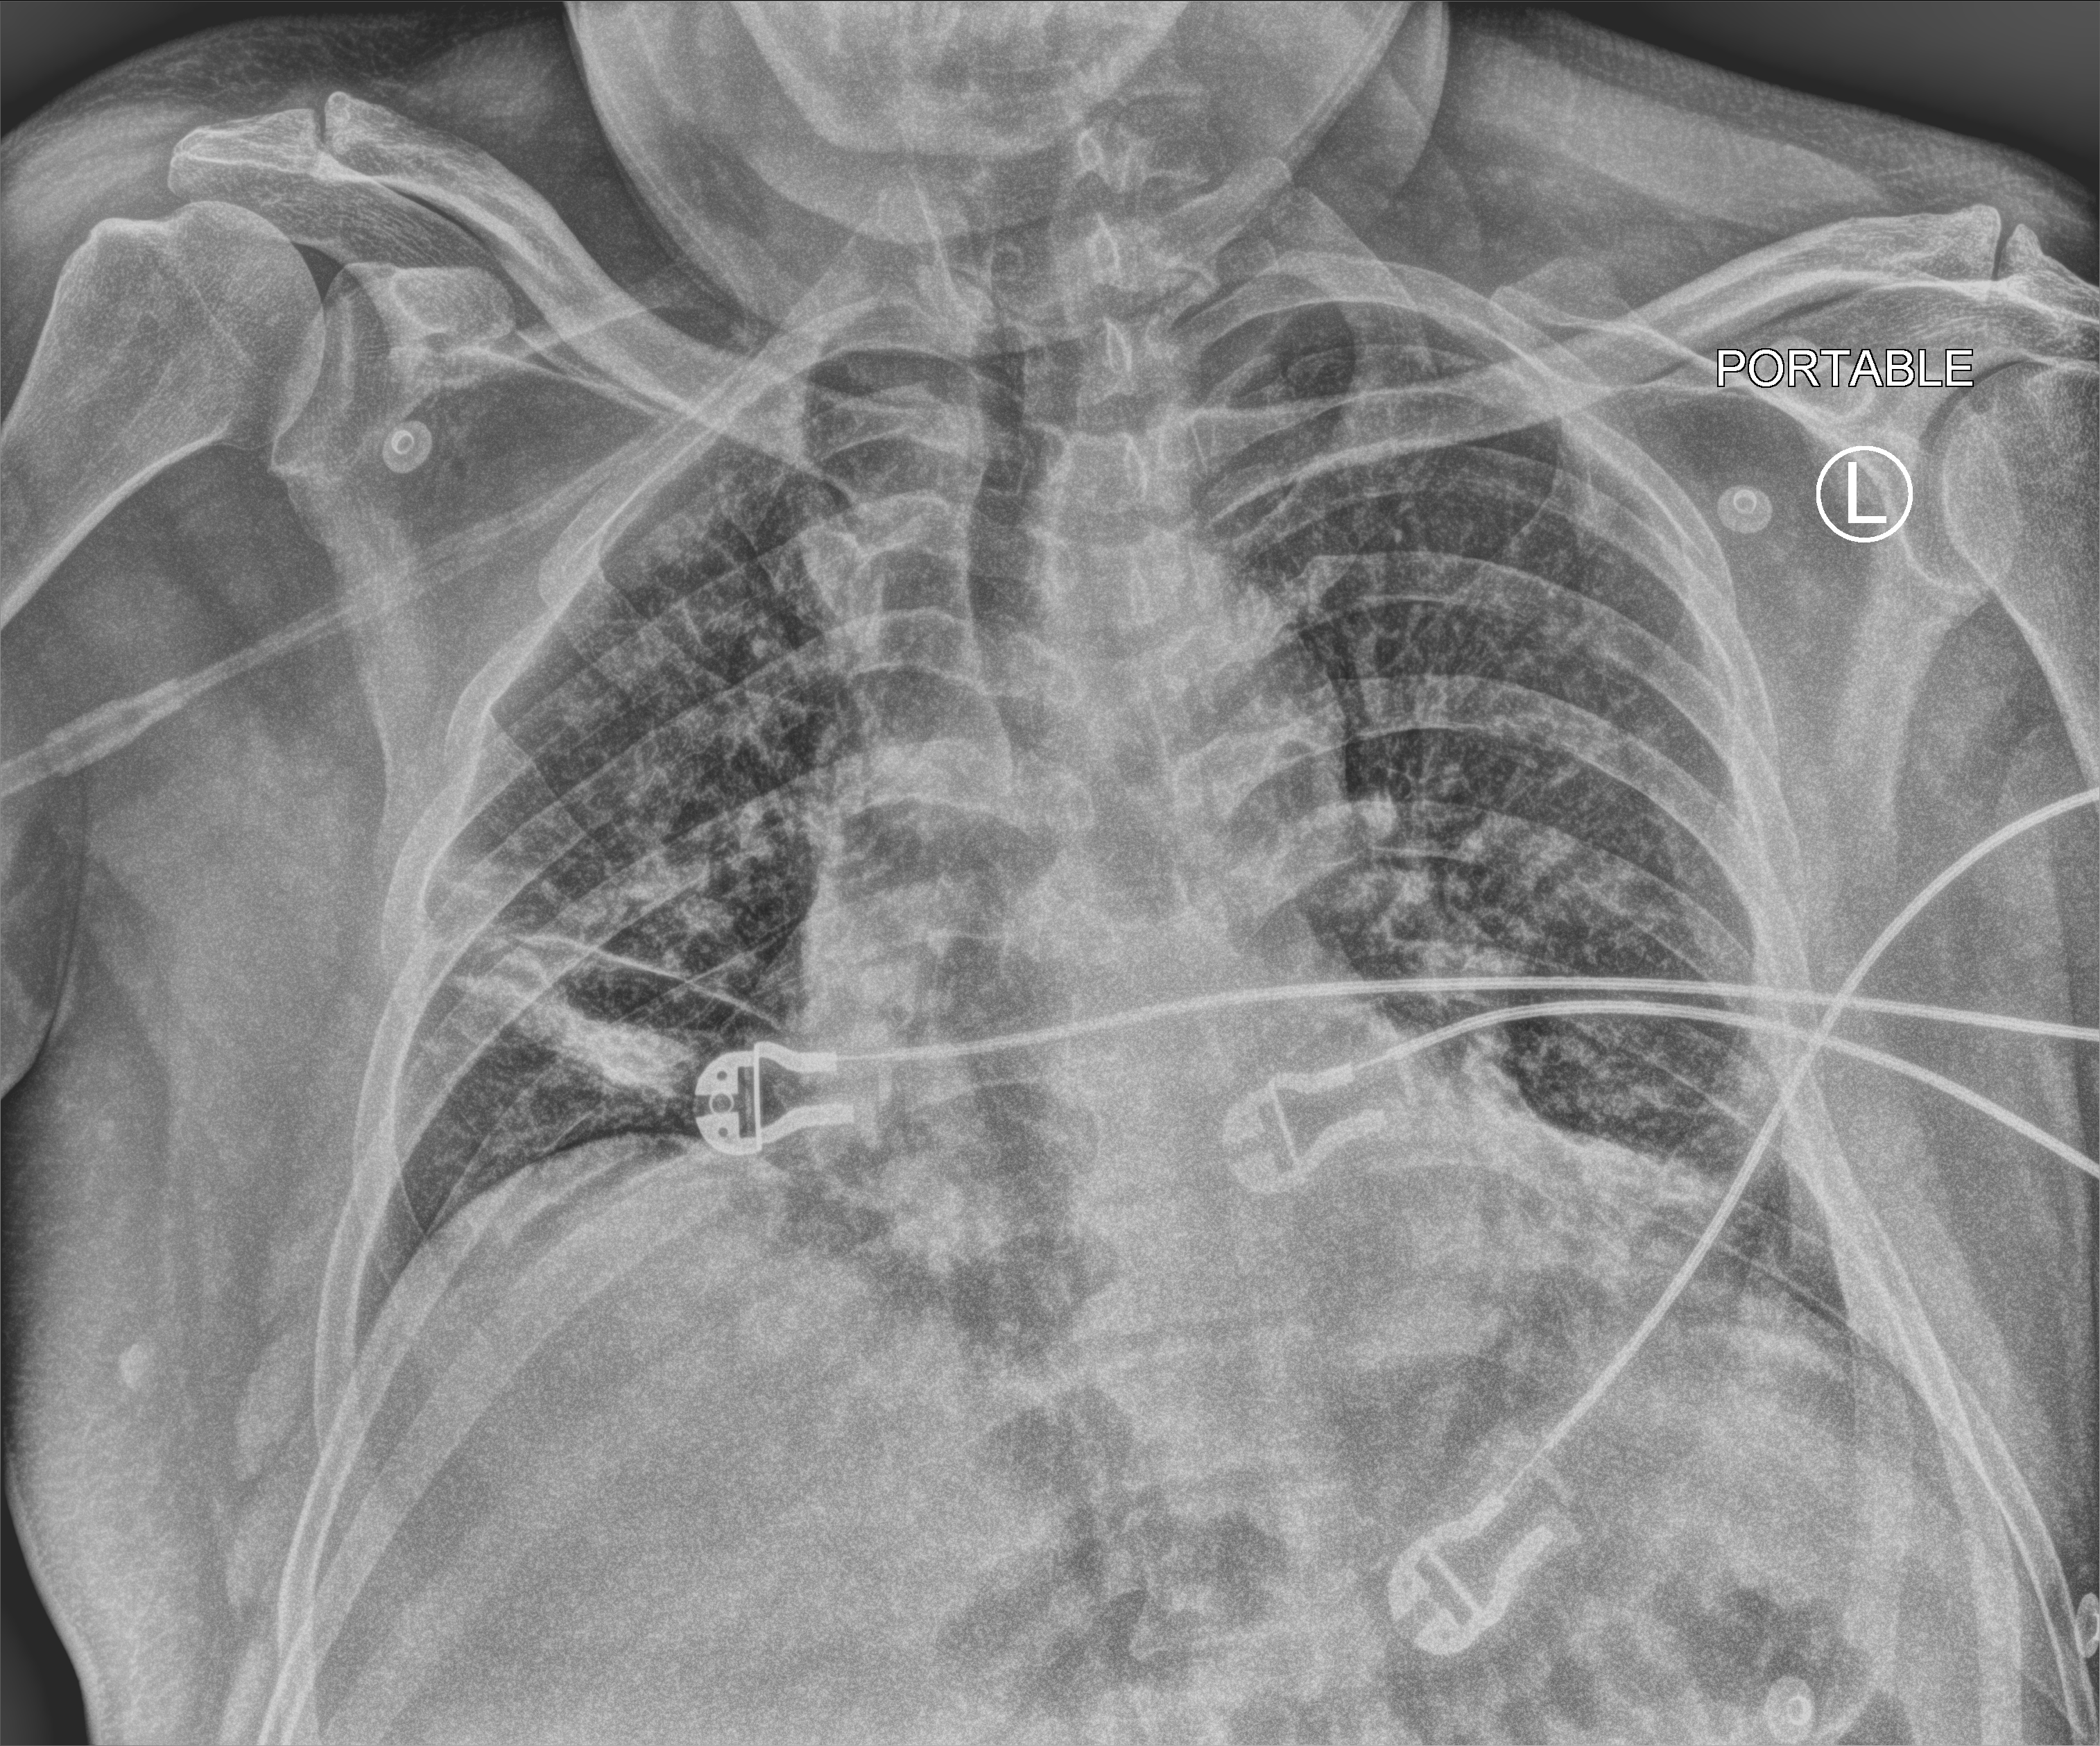
Chest X-ray (portable), anteroposterior (AP) projection. Patient hospitalised with COVID-19; male, aged 18–59 years.
Hospital-stay facts (about this admission, not read from this image; timing relative to this image not recorded):
- mechanically ventilated during this hospital stay: no
- admitted to intensive care during this hospital stay: no